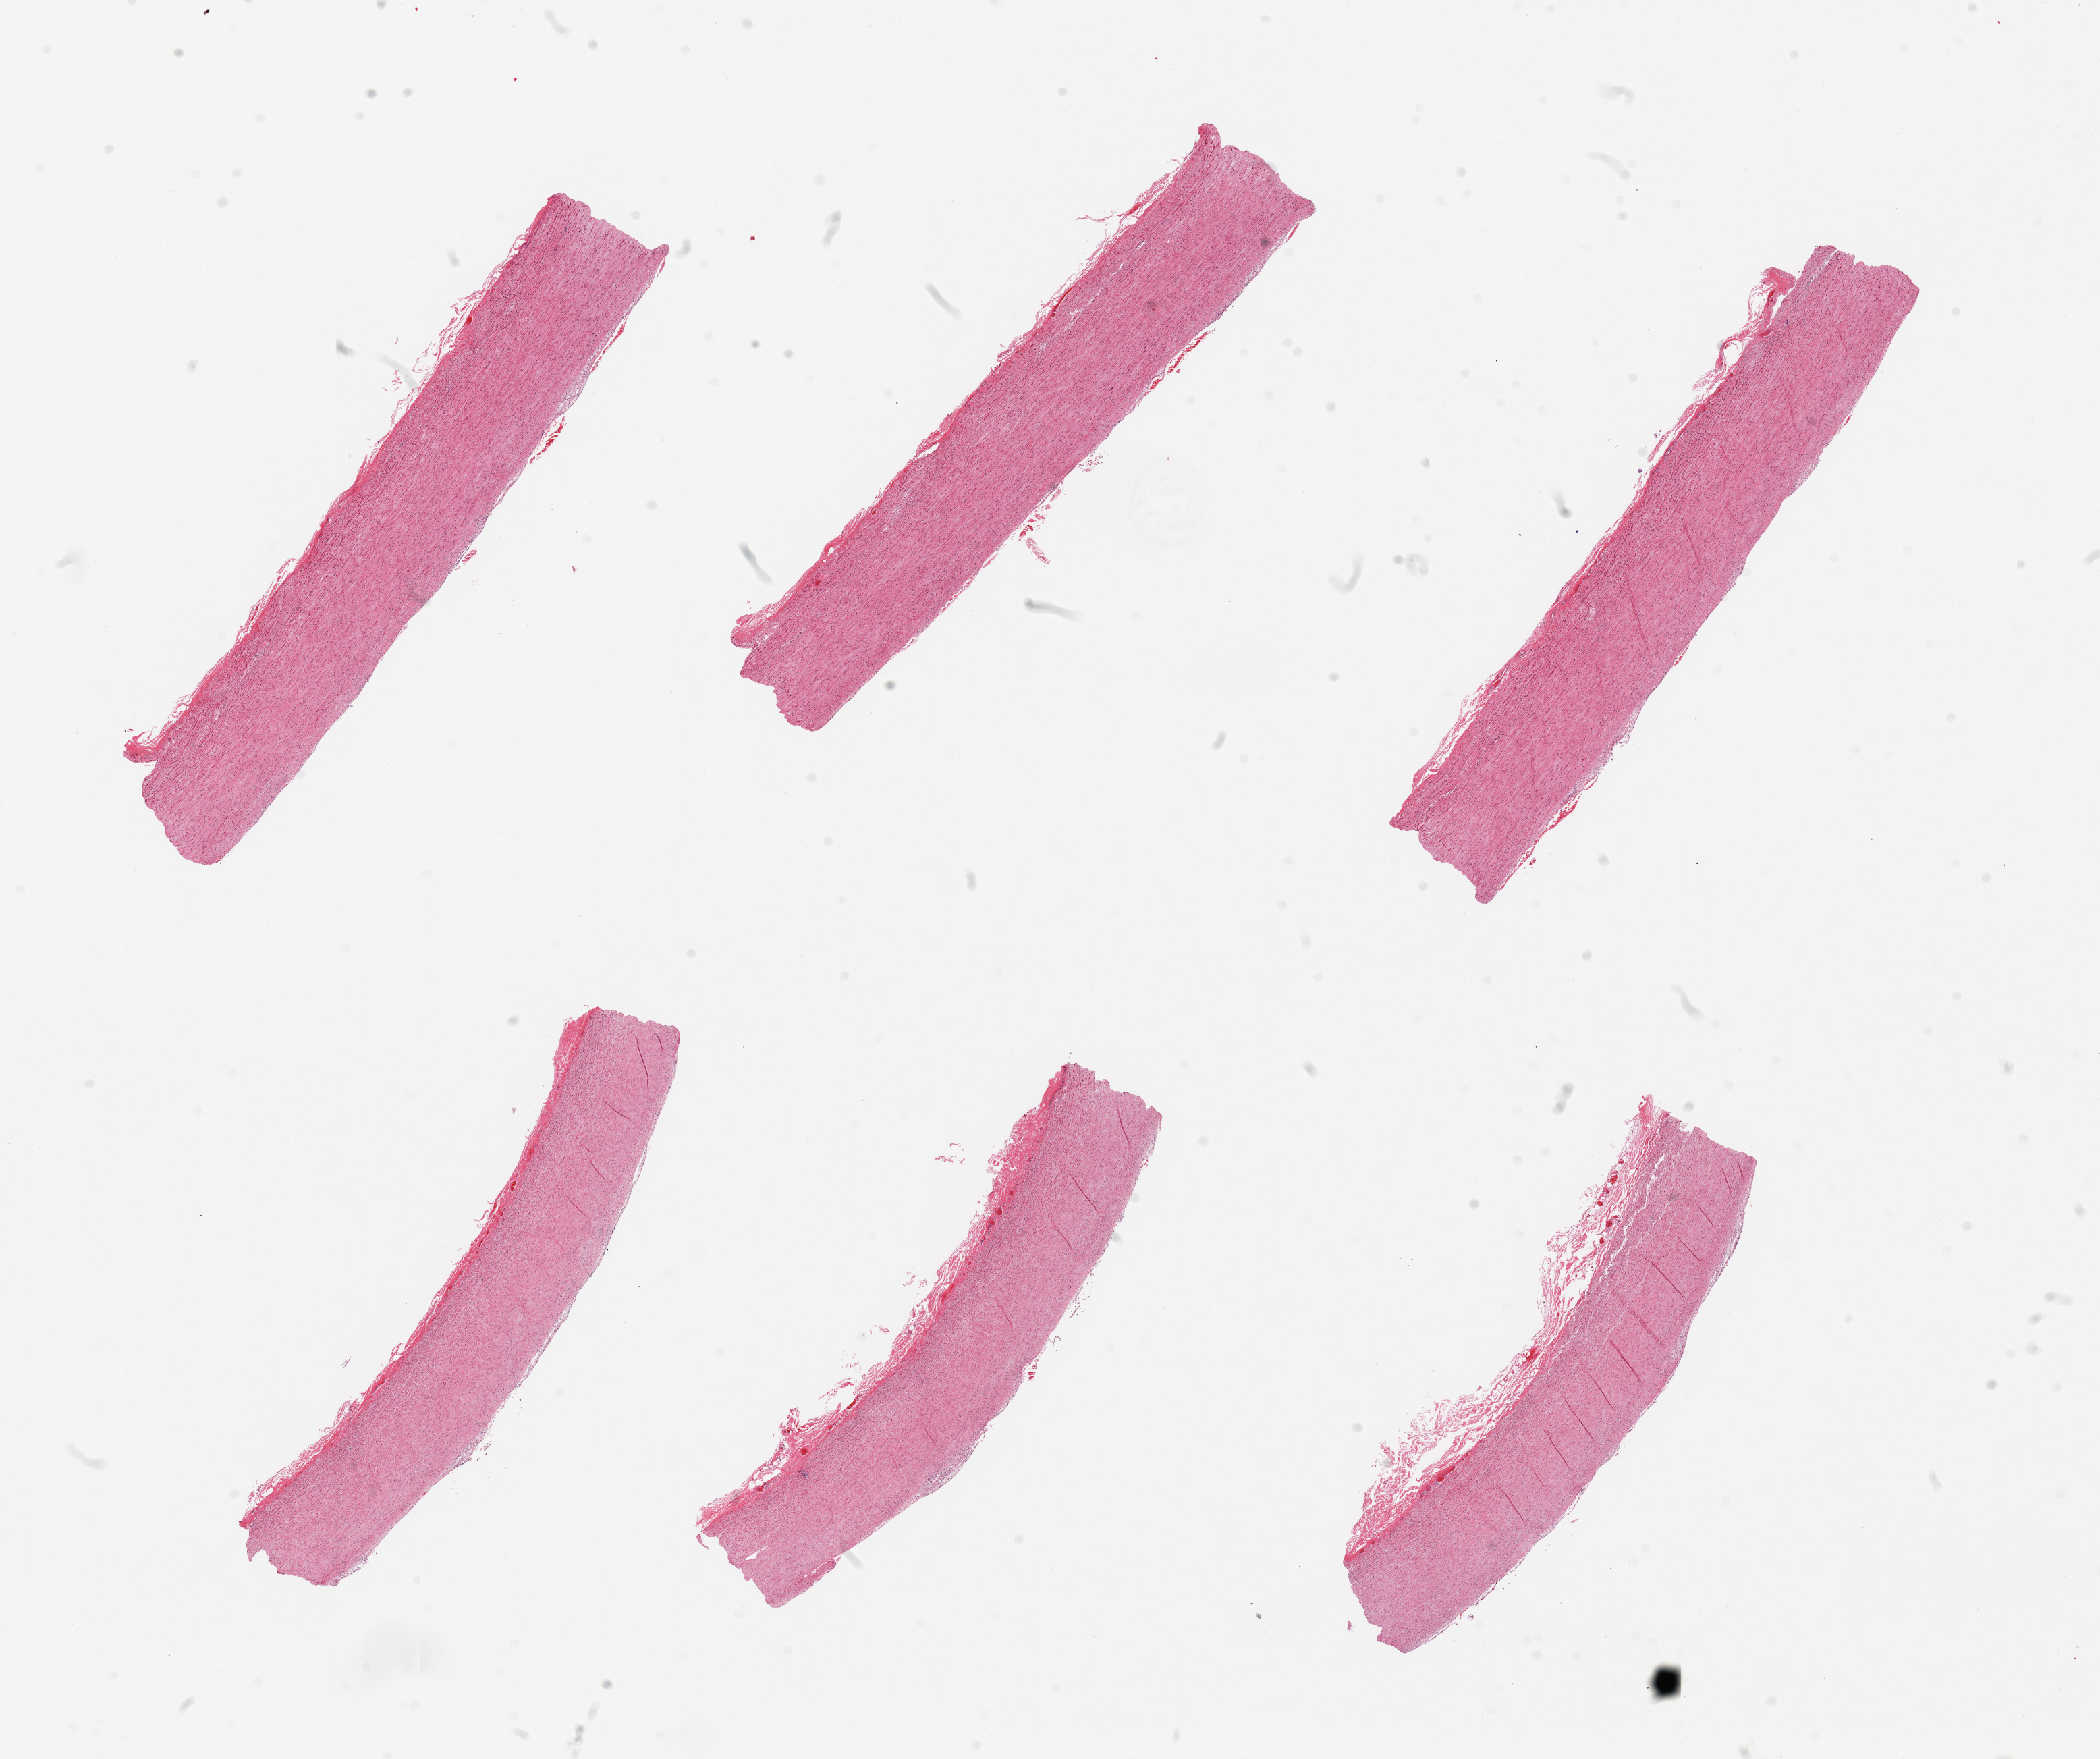
Digitized hematoxylin and eosin (H&E)-stained section — low-resolution overview of the scanned area, about 24.6 x 20.6 mm (from a 20x scan), PAXgene-fixed paraffin-embedded (PFPE) section, section of aorta (target tissue), donor tissue sample. Donor sex: male.
- pathologist's review note for this sample: 6 pieces; well trimmed, plaque free